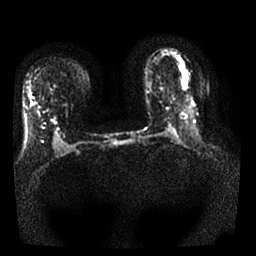
Breast MRI, one axial slice. Position 13 of 25 along the scan axis. Diffusion-weighted series; image 2 of 4 stored at this slice position (different b-values; order by instance number). 1.5 T. 4 mm slice thickness. 256 × 256 image matrix. Female patient.
Structures marked on this image (outlined manually by an expert reader):
- tumour on diffusion-weighted imaging: bounding box <185,80,187,87> (left, top, right, bottom; pixels)